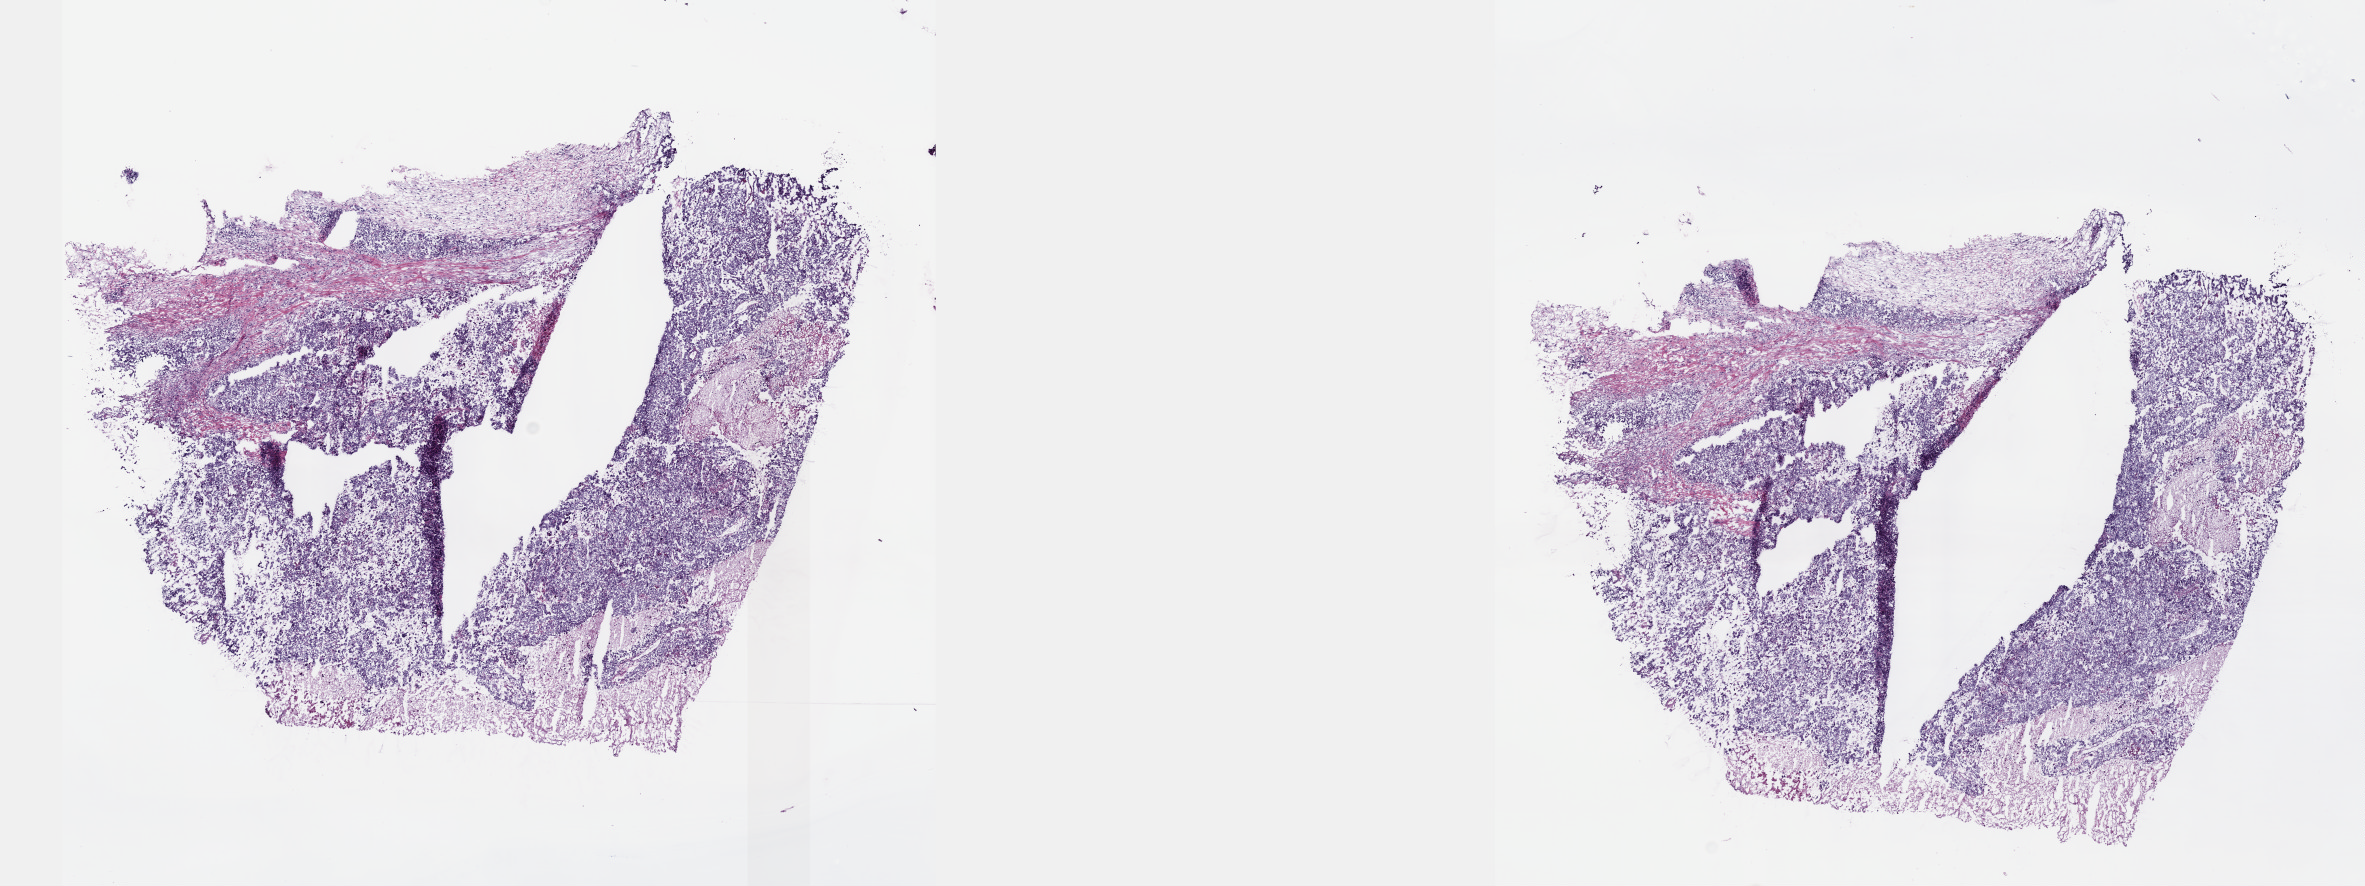
H&E-stained whole-slide image — shown as a low-resolution overview of the whole scanned area (about 19.1 x 7.2 mm, acquisition: 40x scan), frozen section, testis, primary tumour sample. Male, age 21 years at initial diagnosis. Slide review estimates, as recorded: tumour cells 75%, tumour nuclei 75%, normal cells 0%, stromal cells 17%, necrosis 8%. Infiltration values recorded for this section: lymphocyte infiltration 2%, monocyte infiltration 1%, neutrophil infiltration 2%.
Diagnosis: Embryonal carcinoma, NOS. AJCC pathologic stage: IS (6th edition).